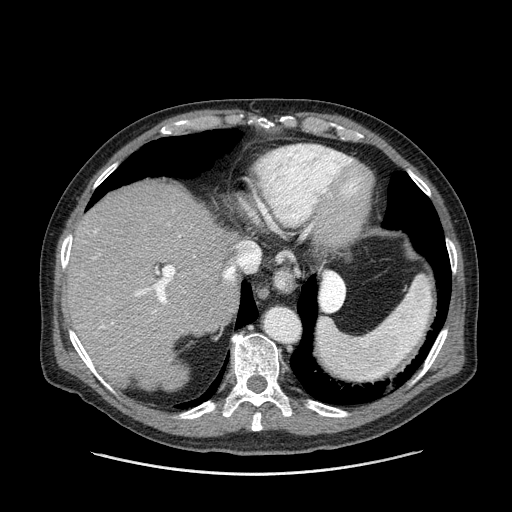
Contrast-enhanced abdominal CT (liver protocol), one axial slice. Slice 114 of 180 in the series (ordered by position). Reconstruction kernel STANDARD. One of 2 acquisitions stored at this slice position. Soft-tissue window (W 400 / L 40 HU). 512 × 512 image matrix, field of view 420 × 420 mm. Case-level facts recorded for this patient, not image findings: diagnosis: hepatocellular carcinoma (patient treated with transarterial chemoembolisation; whether this scan precedes or follows treatment is not stated here); TNM stage (as recorded): Stage-II; Child-Pugh class: A; tumour differentiation: well differentiated; tumour nodularity: multinodular.
Annotated regions visible in this slice (semi-automatic segmentation, software-assisted and operator-edited):
- liver parenchyma outside the tumour (the mass and vessels are separate outlines, so this box may not span the whole liver): box from (x=66, y=182) to (x=238, y=390) px
- liver vessels: (x=90, y=231)–(x=175, y=363)